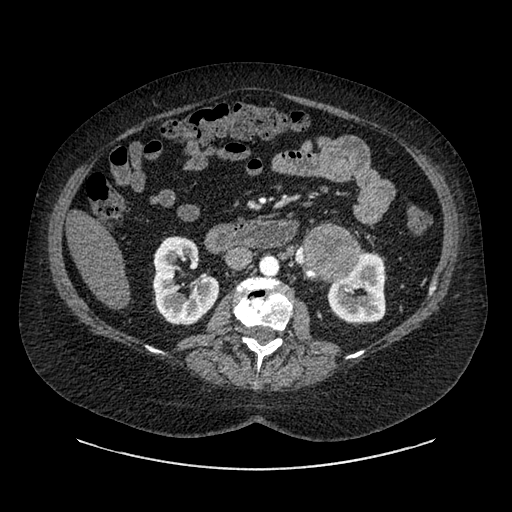
Contrast-enhanced abdominal CT, one axial slice; position 499 of 769 along the scan axis; 120 kVp; intravenous contrast given; soft-tissue window (W 400 / L 40 HU); 0.62 mm slice thickness; 512 × 512 image matrix, field of view 460 × 460 mm. Patient: female, 61 years. Case-level facts recorded for this patient, not image findings: diagnosis: adrenocortical carcinoma; tumour side: left adrenal; tumour size at pathology: 13 cm; Ki-67 index: 79 %; stage (as recorded): 2.
Annotated regions visible in this slice (semi-automatically segmented with operator editing):
- mass: box from (x=306, y=230) to (x=358, y=279) px